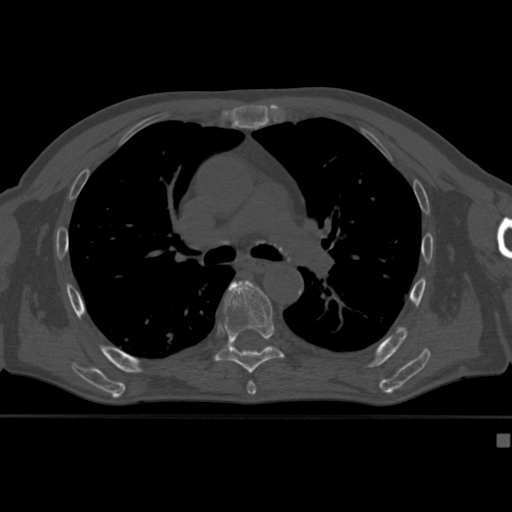
CT including the spine, one axial slice. Position 281 of 430 along the scan axis. 120 kVp. Bone window (W 1800 / L 400 HU). 512 × 512 image matrix. Male patient, age 64 years. Case-level facts recorded for this patient, not image findings: primary cancer: uterus; vertebrae with lytic lesions (as recorded): T1, T4, T5, T7, L5.
Annotated regions visible in this slice (semi-automatic segmentation, software-assisted and operator-edited):
- T7 vertebra: bounding box (x1, y1, x2, y2) in pixels: (214, 280, 285, 374)